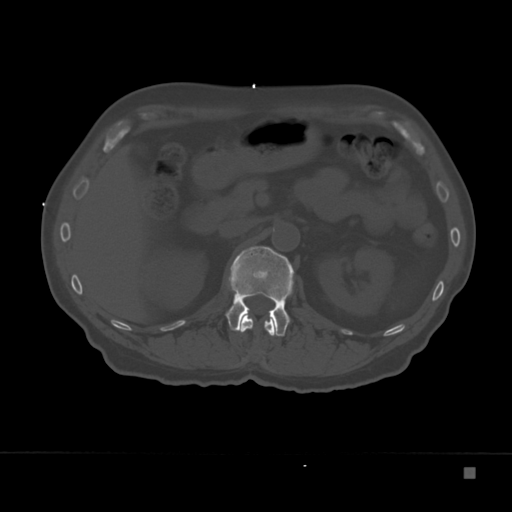
CT including the spine, one axial slice; position 117 of 332 along the scan axis; reconstruction kernel Br40s; bone window (W 1800 / L 400 HU); 1.5 mm slice thickness; 512 × 512 image matrix, field of view 389 × 389 mm. Patient: male, 72 years. Case-level facts recorded for this patient, not image findings: primary cancer: skeletal.
Structures marked on this image (semi-automatic segmentation, software-assisted and operator-edited):
- L1 vertebra: bounding box (x1, y1, x2, y2) in pixels: (225, 246, 295, 337)
- T12 vertebra: (241, 316, 275, 336)